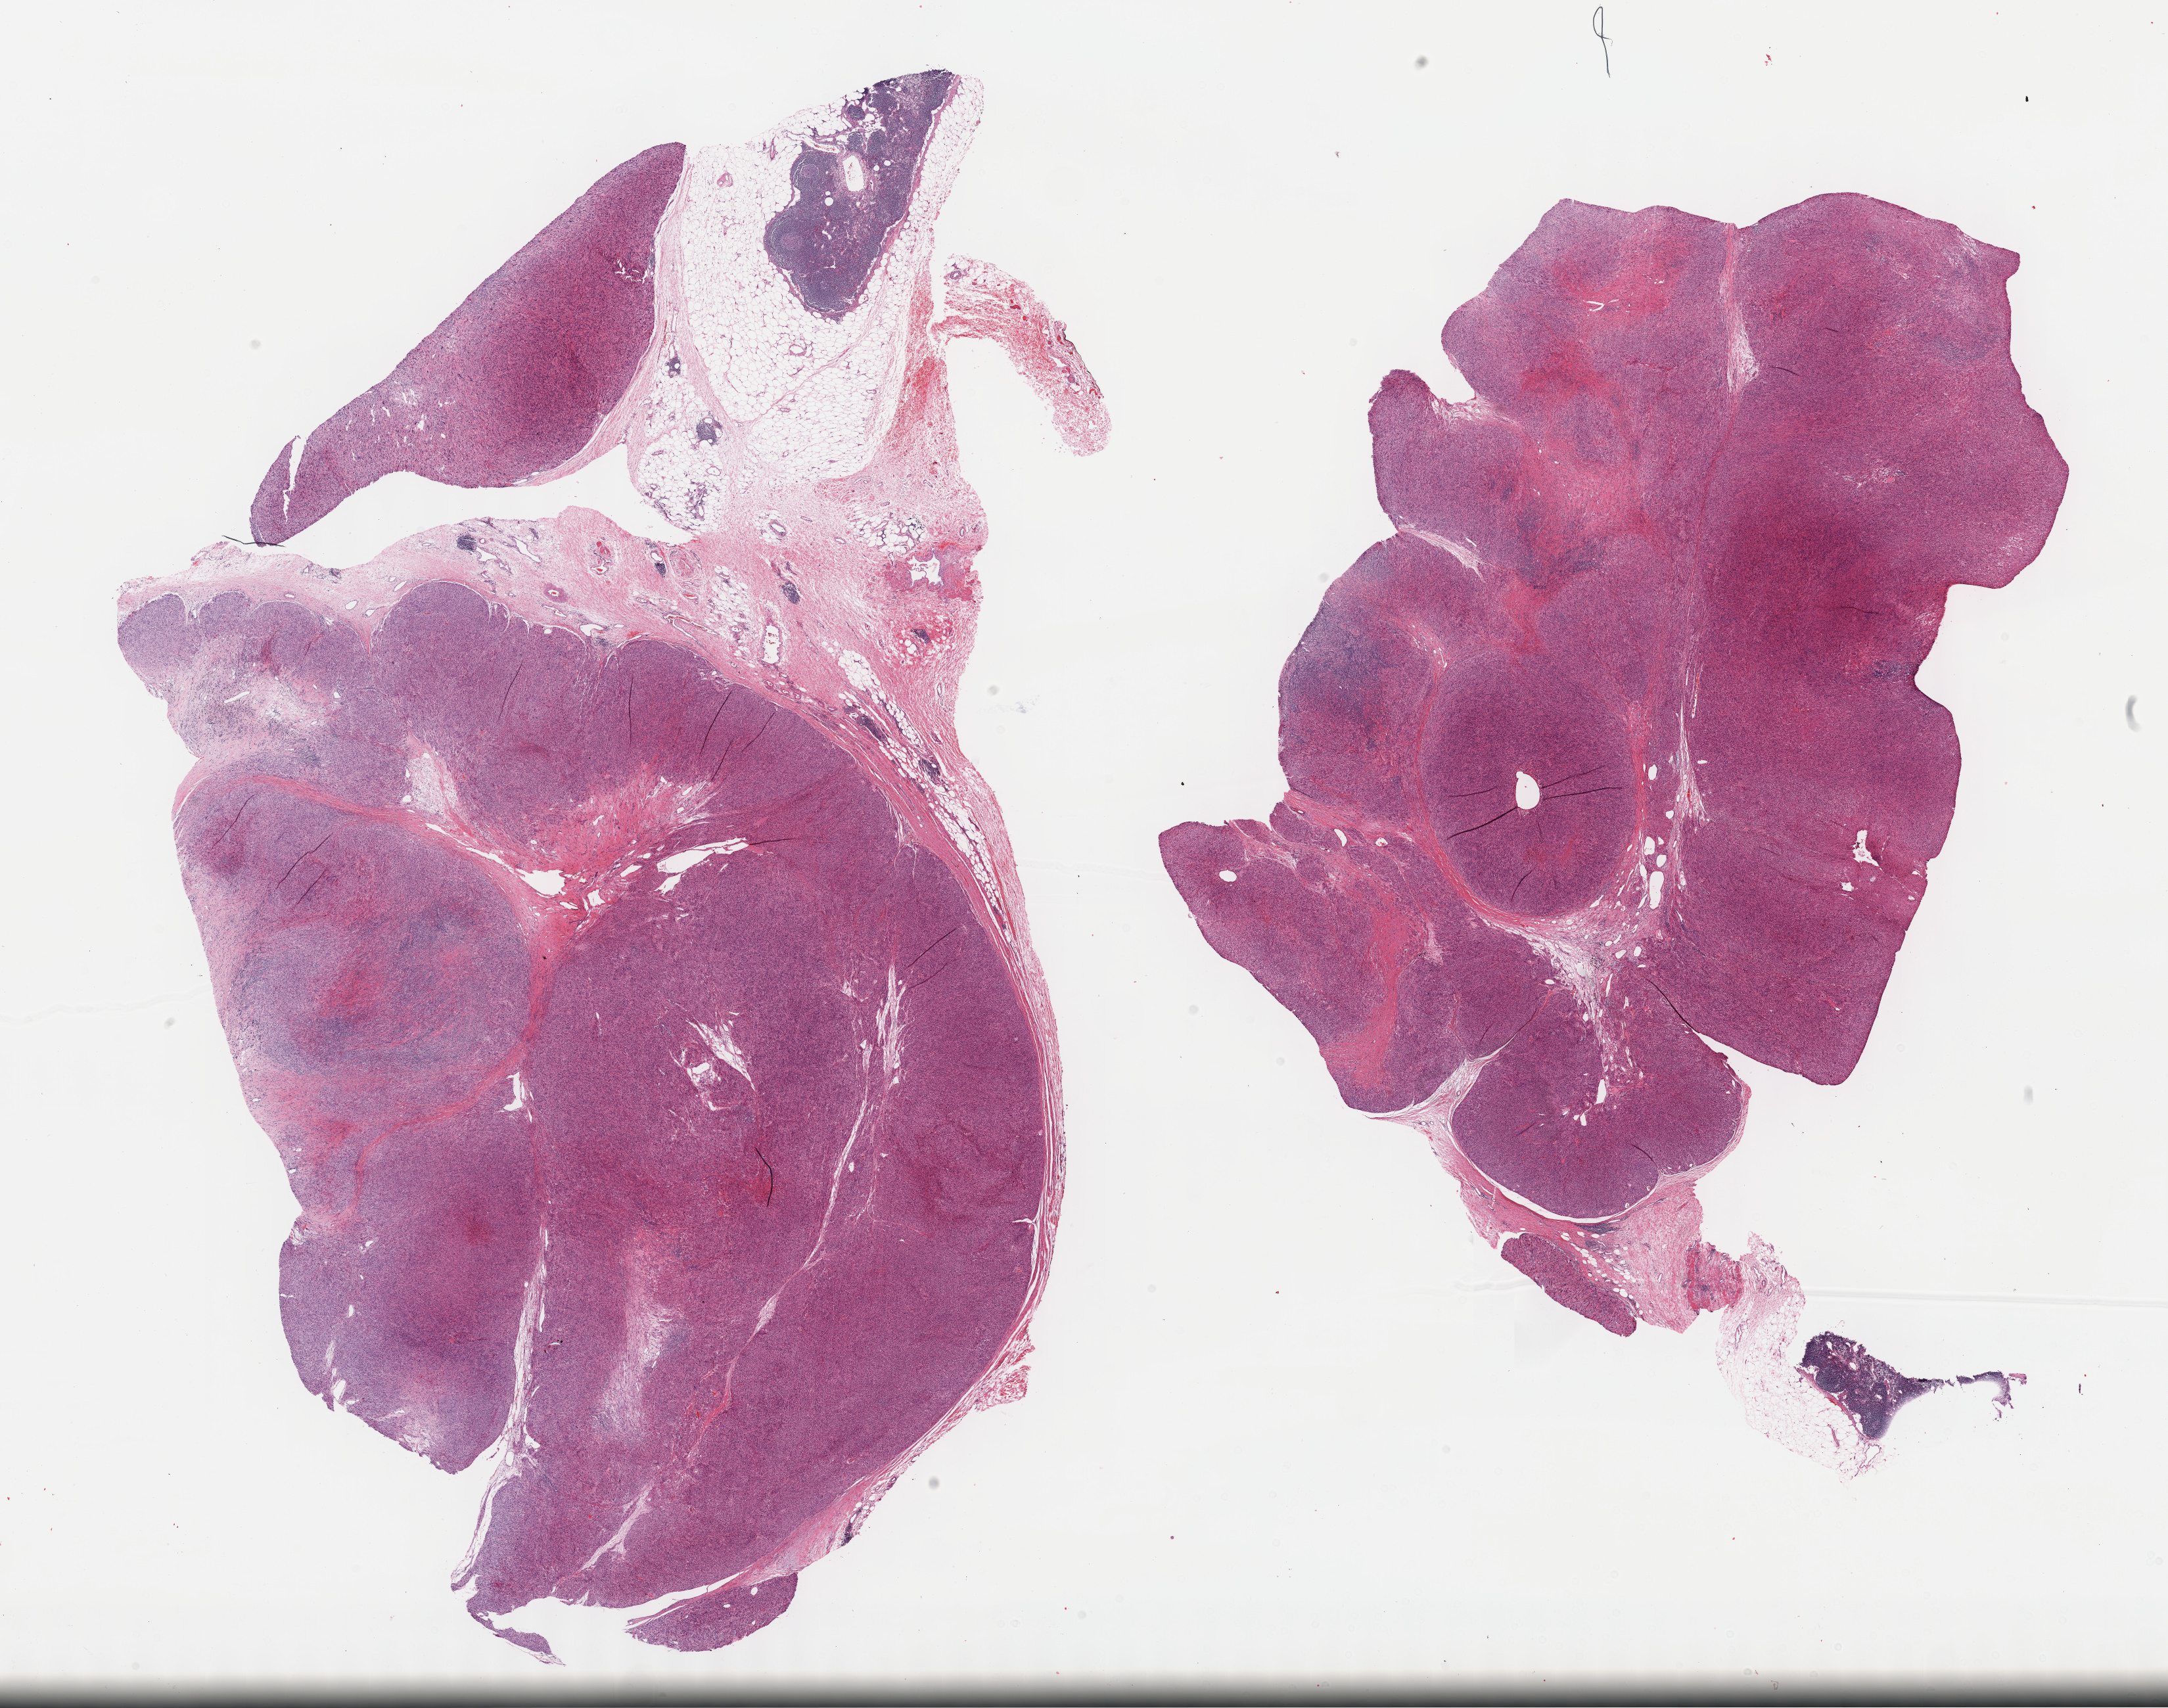
Whole-slide histology image, H&E — low-resolution overview of the scanned area, about 26.7 x 21.0 mm; formalin-fixed paraffin-embedded (FFPE) diagnostic section; sample: primary tumour, retroperitoneum and peritoneum. Male patient; age at initial diagnosis 70 years.
Histologic diagnosis: Leiomyosarcoma, NOS.